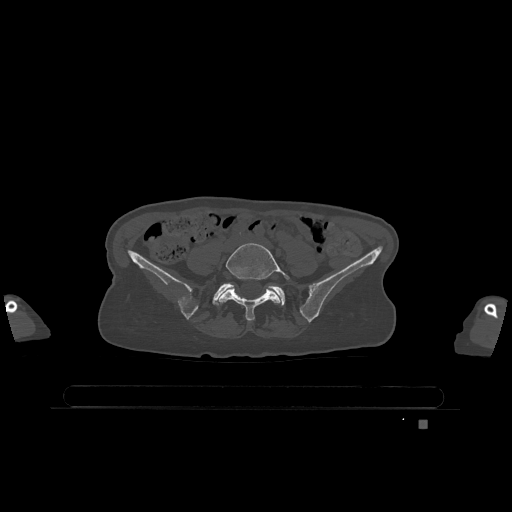
CT including the spine, one axial slice; position 230 of 1317 along the scan axis; bone window (W 1800 / L 400 HU); 512 × 512 image matrix, field of view 500 × 500 mm. Patient: female, 74 years. From the clinical record (not read from this slice): primary cancer: lung; vertebrae with lytic lesions (as recorded): T1, T4, T5, T6, L4, L5.
Annotated regions visible in this slice (semi-automatically segmented with operator editing):
- L5 vertebra: bounding box (x1, y1, x2, y2) in pixels: (217, 243, 290, 321)